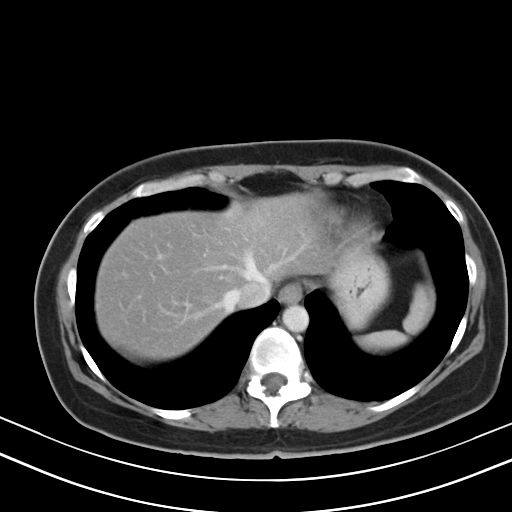
Contrast-enhanced abdominal CT, one axial slice; position 41 of 47 along the scan axis; 130 kVp; intravenous contrast given; soft-tissue window (W 400 / L 40 HU); 5 mm slice thickness; 512 × 512 image matrix, field of view 350 × 350 mm. Female patient. Case-level facts recorded for this patient, not image findings: diagnosis: colorectal cancer liver metastases, imaged before liver resection; multiple liver metastases: no; largest metastasis: 3.5 cm; disease in both lobes: no.
Structures marked on this image (outlined manually by an expert reader):
- hepatic veins: box from (x=214, y=248) to (x=301, y=311) px
- liver: (x=96, y=201)–(x=323, y=357)
- planned liver remnant (the part of the liver to remain after resection): (x=96, y=201)–(x=324, y=357)
- portal vein (with intrahepatic branches): (x=217, y=267)–(x=272, y=306)